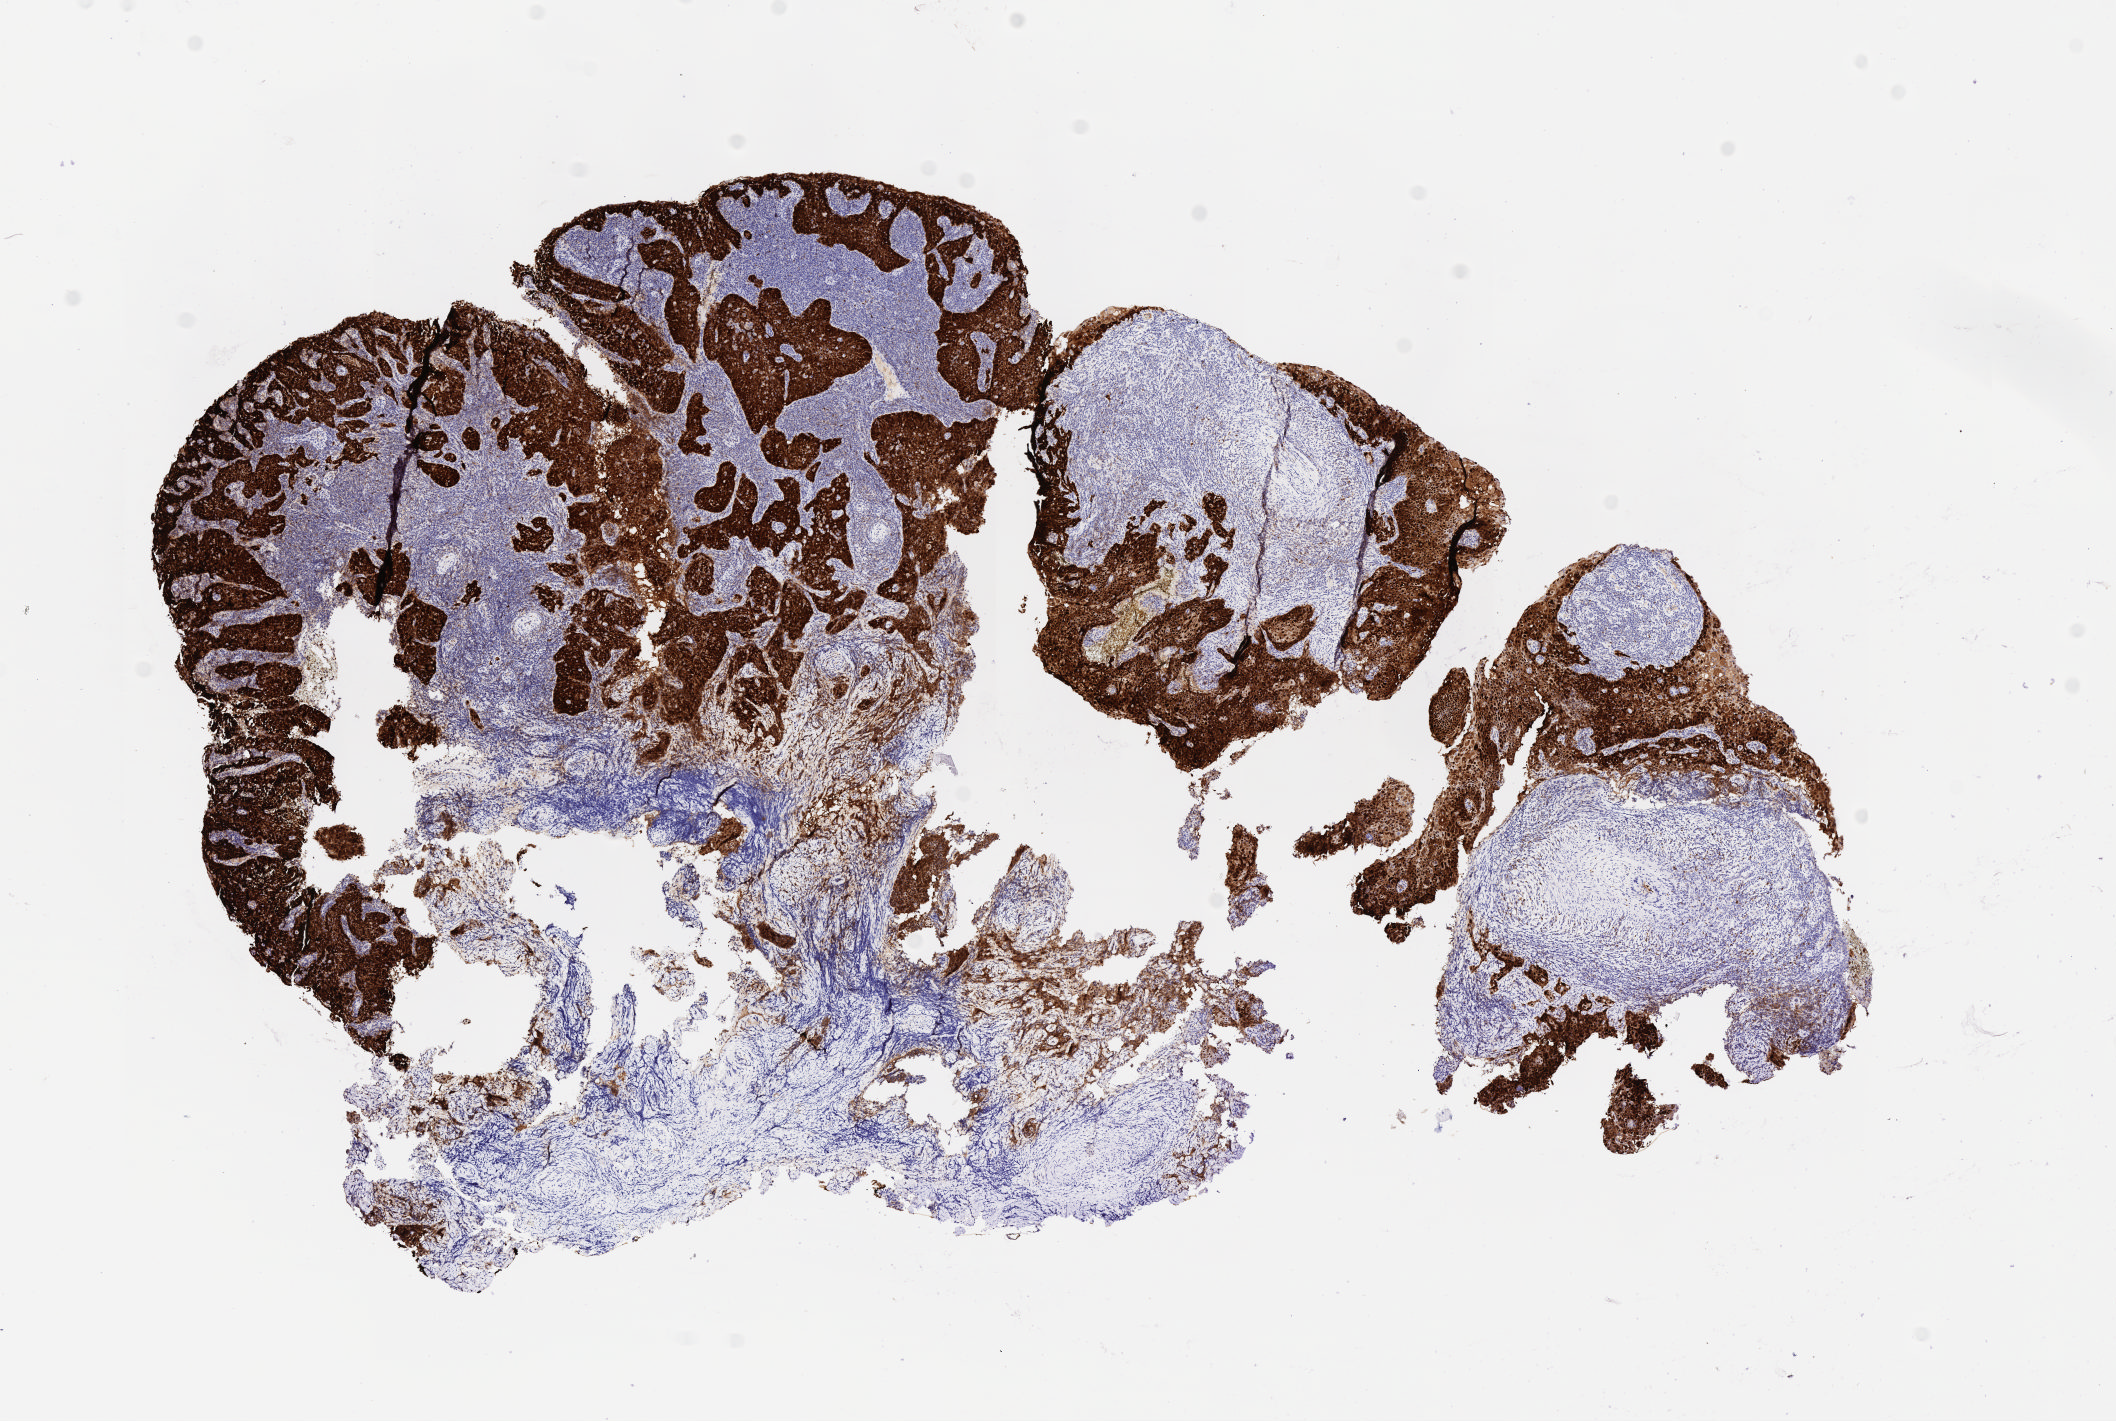
Immunohistochemistry (IHC) whole-slide image stained for p16 (p16INK4a), a low-resolution overview of the entire scanned area, about 8.6 x 5.7 mm, specimen: tumor tissue, anatomic site: cervix. Patient female; 43 years old.
Histologic diagnosis: Squamous cell carcinoma, keratinizing, NOS.